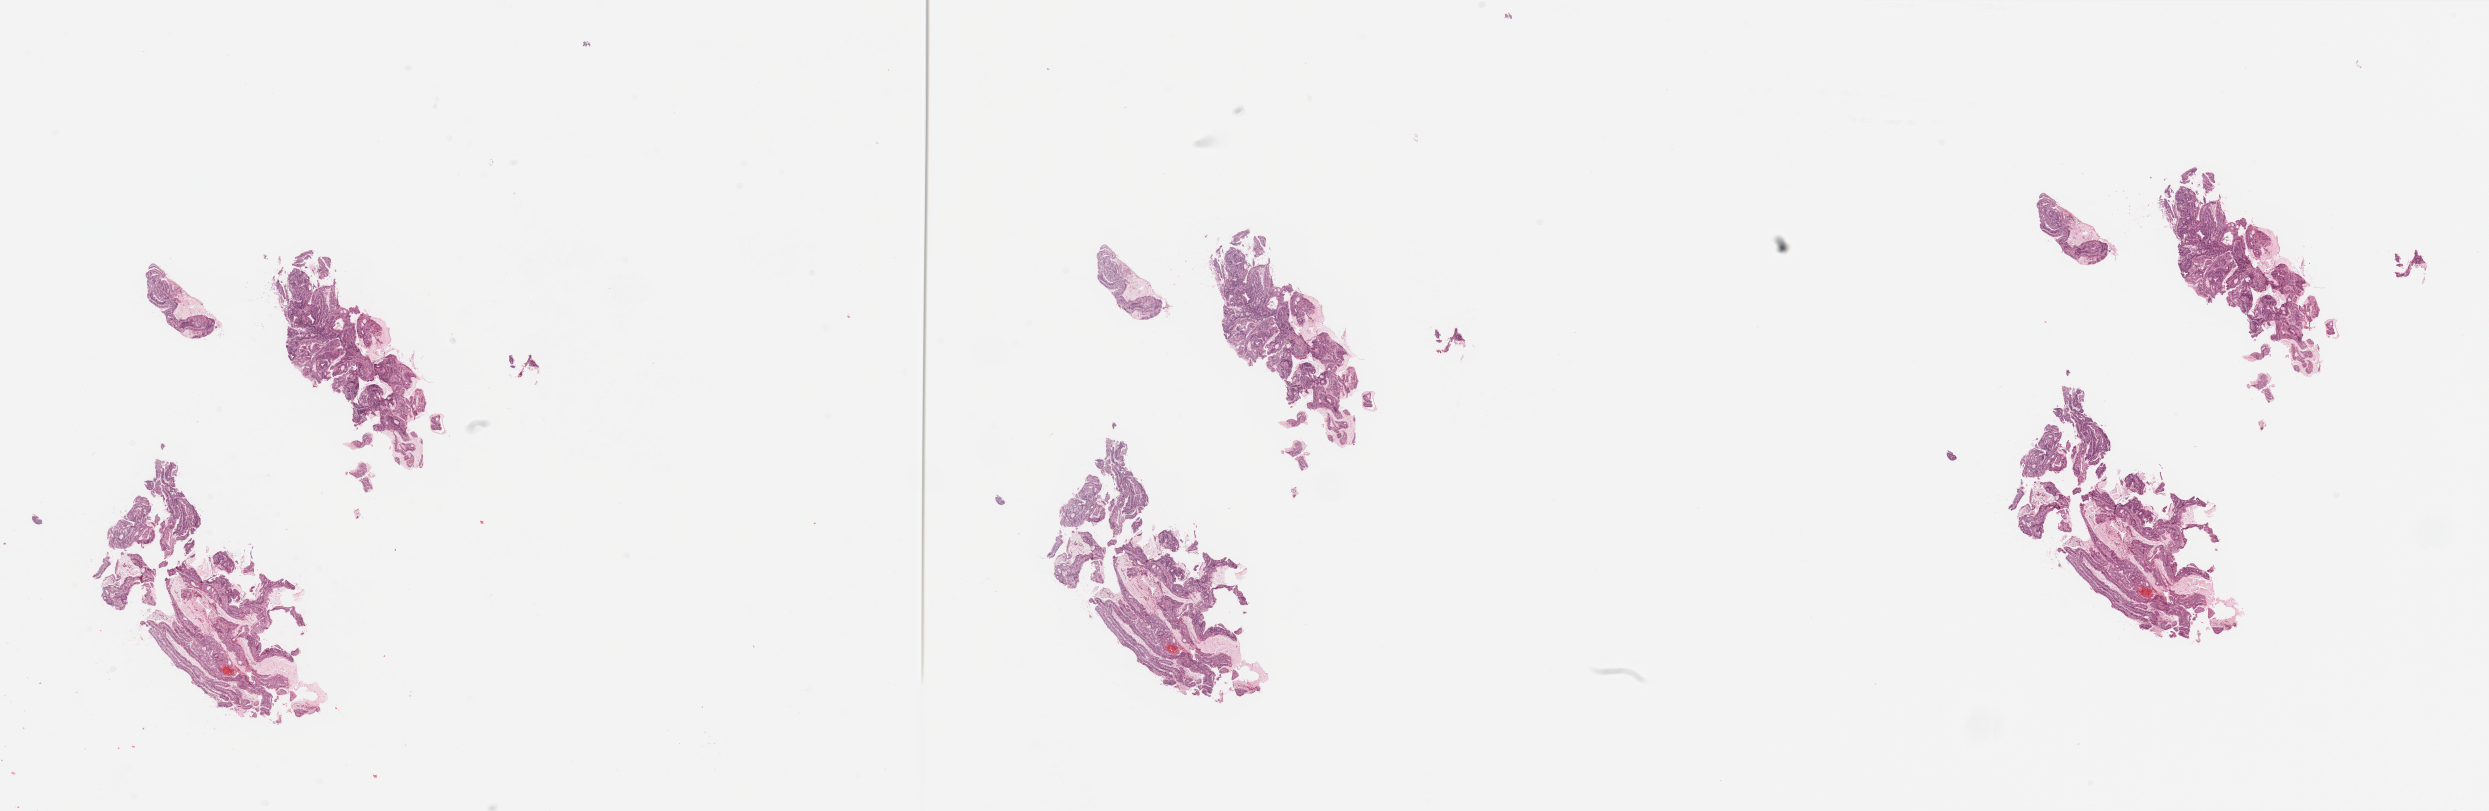
Digitized H&E tissue section (whole slide), a low-resolution overview of the entire scanned area, about 39.4 x 12.8 mm; uterus, tumour tissue. Female, 53 y/o. Histologic grade: G1 (well differentiated).
Histologic diagnosis: Endometrioid adenocarcinoma, NOS. AJCC pathologic stage: III. Primary tumour site (as recorded): anterior endometrium.